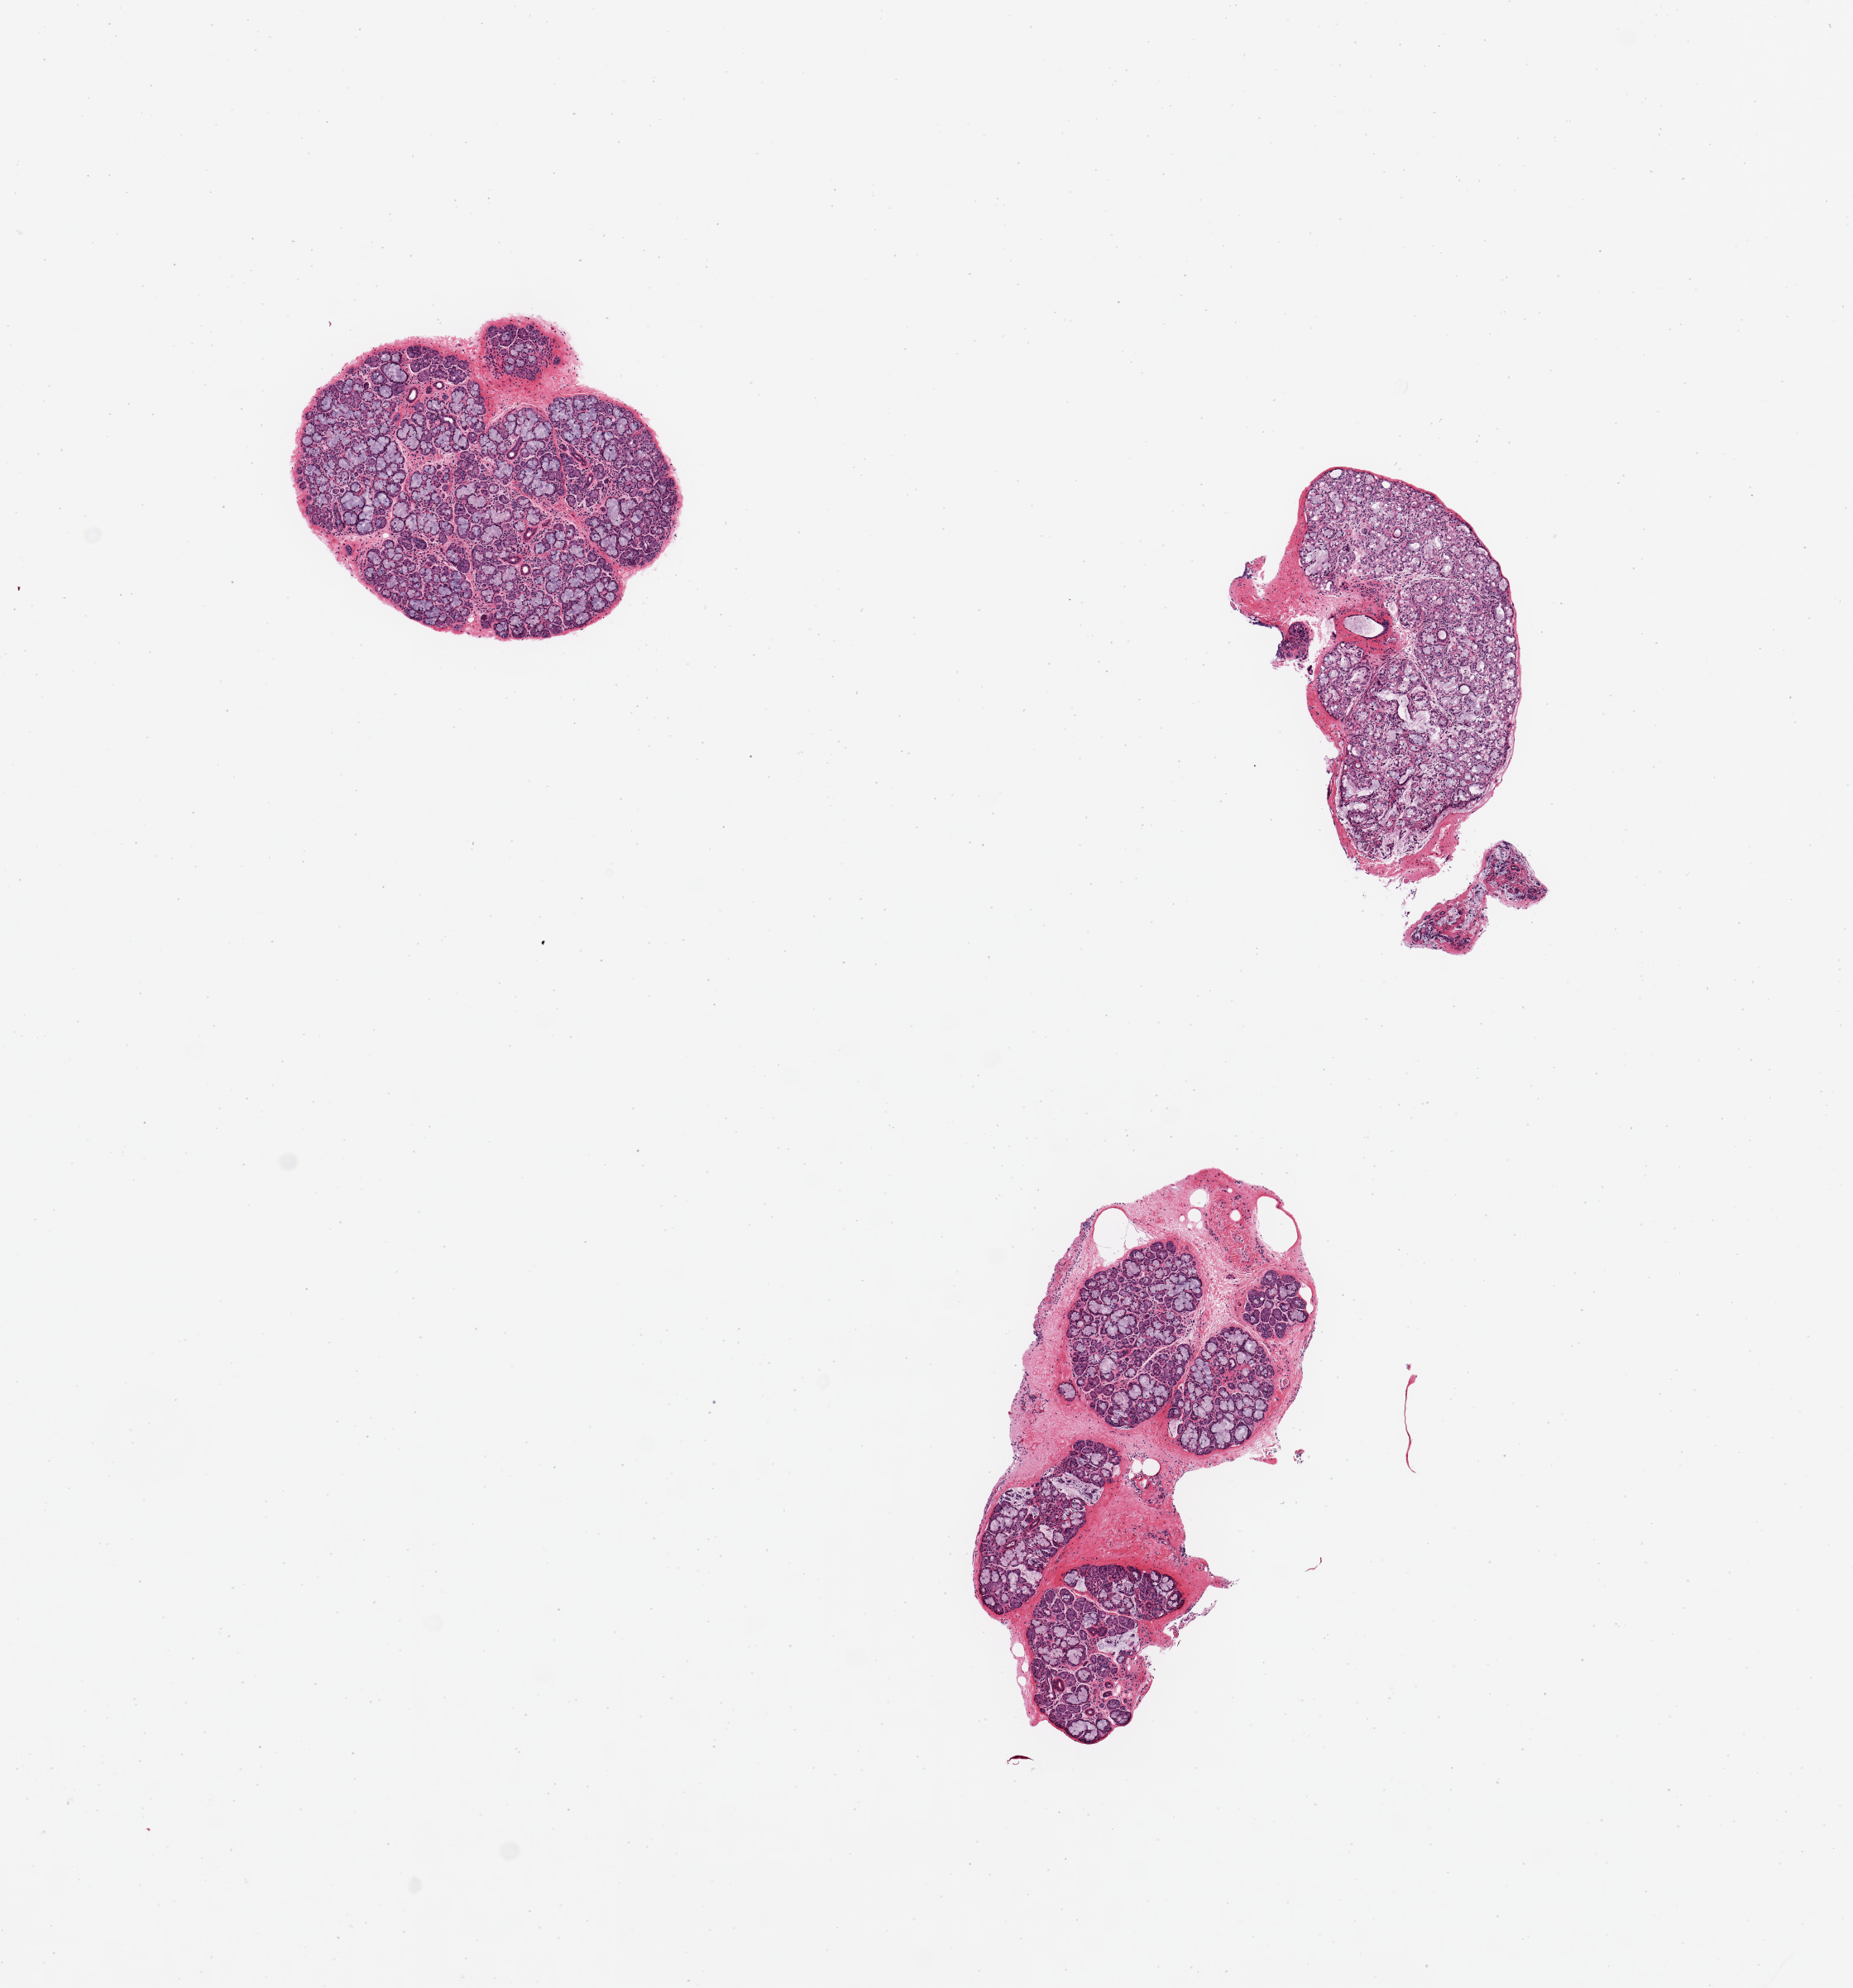
Whole-slide image, haematoxylin and eosin stain, low-resolution overview of the scanned area, about 8.9 x 9.5 mm, PAXgene-fixed paraffin-embedded (PFPE) section, target tissue: minor salivary gland, tissue donor sample.
Reviewer comment on this tissue sample: 3 pieces, ~80% gland/duct parenchyma; rest is gland stroma.